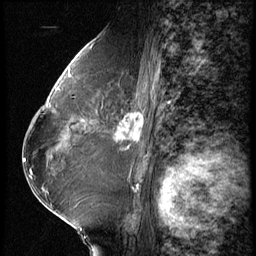
Breast MRI (dynamic contrast-enhanced), one sagittal slice. Slice 33 of 62 in the series (ordered by position). 3 images stored at this slice position (order not interpretable as contrast timing). 1.5 T. TE 4.2 ms, TR 9 ms. 2.5 mm slice thickness. 256 × 256 image matrix. Female patient, age 65 years. Case-level facts recorded for this patient, not image findings: setting: breast cancer imaged before/during neoadjuvant chemotherapy; receptor status: HR-positive, HER2-negative.
Outlined on this slice (semi-automatic segmentation, software-assisted and operator-edited):
- analysis volume of interest (the breast-tissue region the enhancement analysis was run in; not a lesion): bounding box (x1, y1, x2, y2) in pixels: (104, 104, 154, 161)
- tumour enhancement mask (voxels above the 140 % enhancement threshold inside the analysis volume of interest): (116, 112, 144, 141)